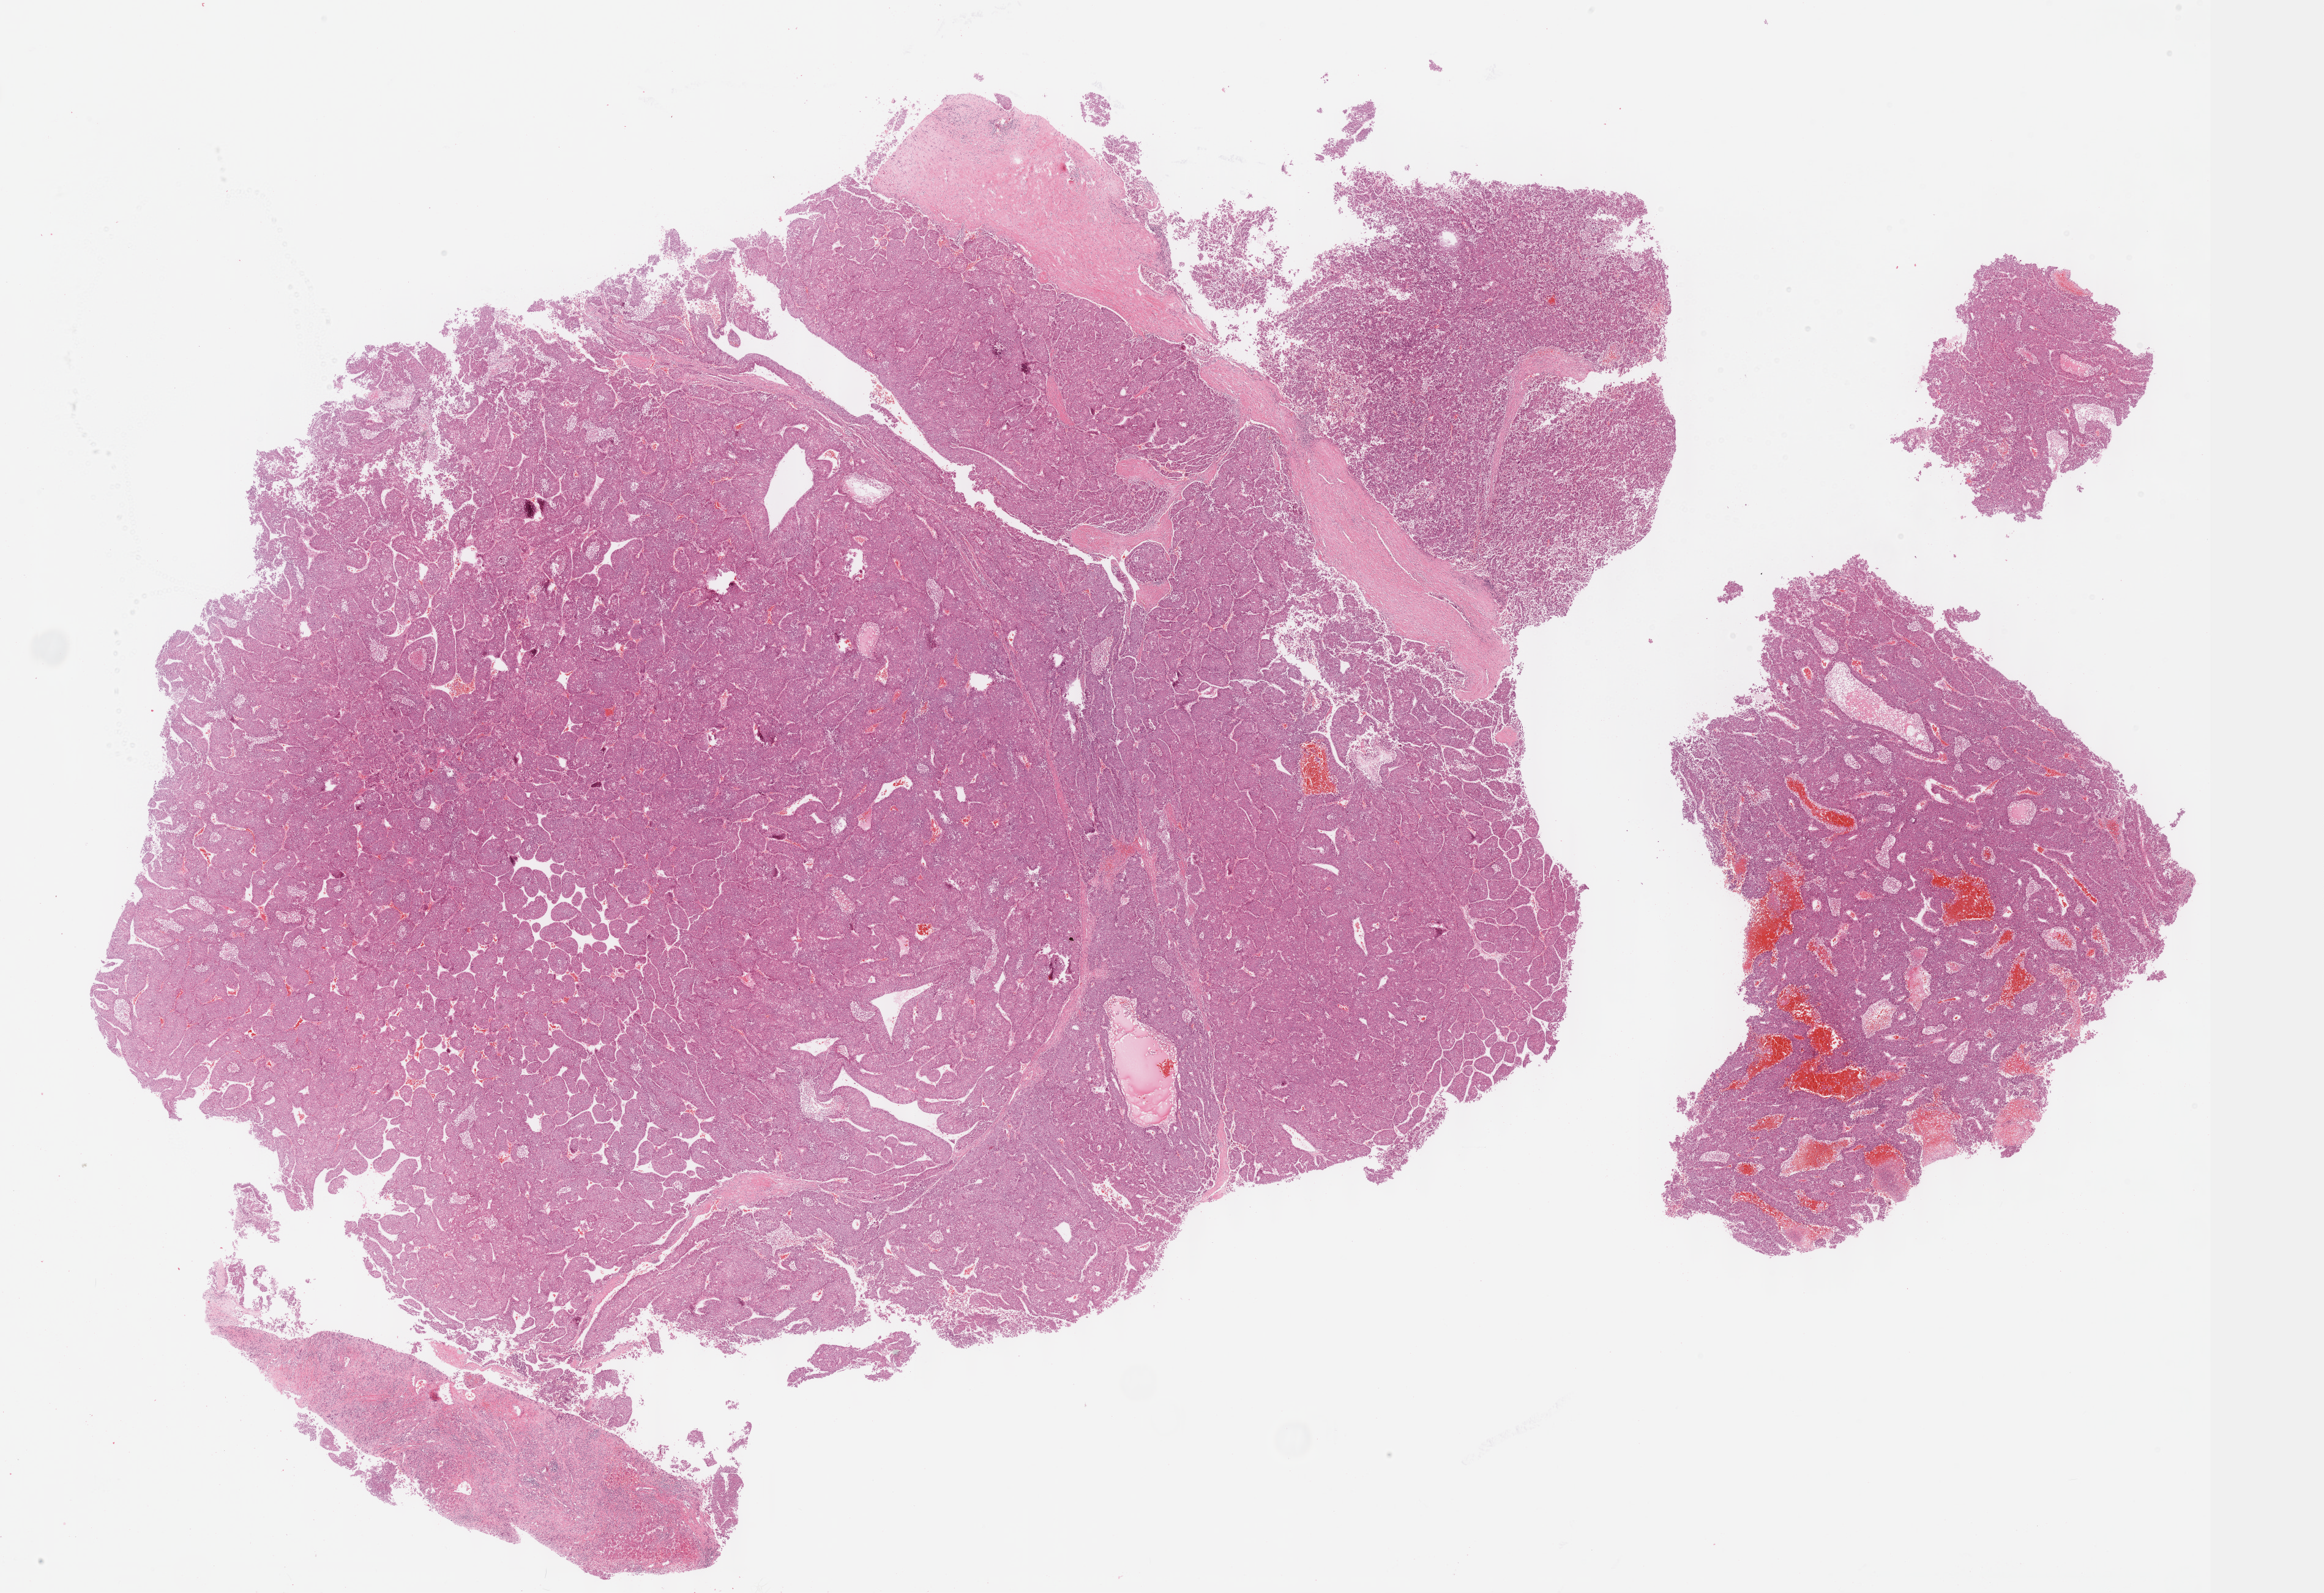
H&E-stained whole-slide image, a low-resolution overview of the entire scanned area, about 30.7 x 21.0 mm (acquisition: 40x scan); formalin-fixed paraffin-embedded (FFPE) diagnostic section; liver, primary tumour sample. Patient: male, age at initial diagnosis 74 years. Histologic grade: G2 (moderately differentiated).
Histologic diagnosis: Hepatocellular carcinoma, NOS. AJCC pathologic stage: I (7th edition). TNM: T1 NX M0.